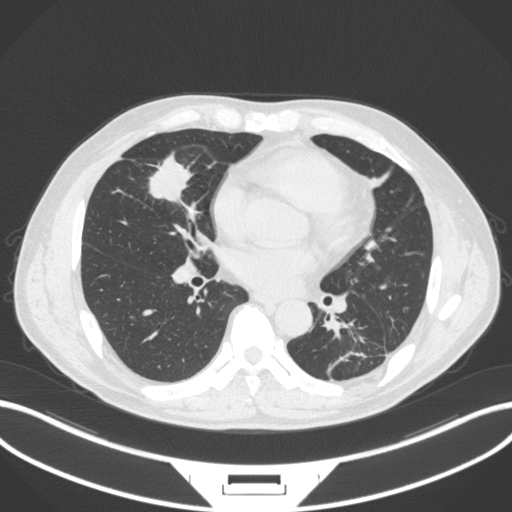
Chest CT, one axial slice. 120 kVp. Lung window (W 1500 / L -600 HU). 1 mm slice thickness. 512 × 512 image matrix, field of view 400 × 400 mm. Male patient, age 59 years. From the clinical record (not read from this slice): clinical TNM (as recorded): T2a N1 M0.
Annotated regions visible in this slice (bounding box drawn by a radiologist):
- lung tumour (recorded histology: adenocarcinoma): bounding box (x1, y1, x2, y2) in pixels: (141, 153, 198, 207)